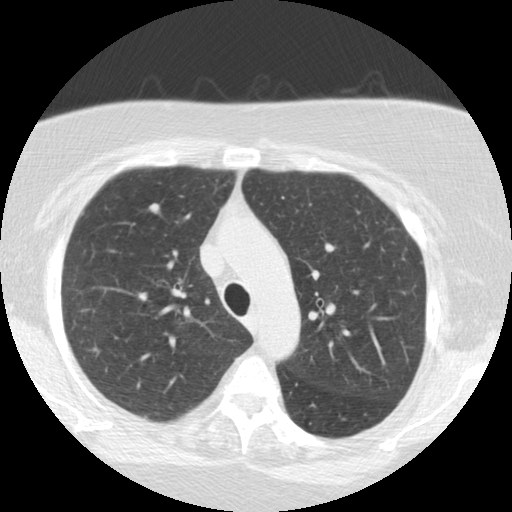
Chest CT (low-dose screening protocol), one axial image. Second annual screen. Lung window (W 1500 / L -600 HU). Slice 171 of 225 in the series. 512 × 512 image matrix. Female participant, aged 64 years at enrolment.
Lesion marked by an expert reader, box from (x=128, y=193) to (x=170, y=230) px. The exam's reader record, not a measurement of the box and not confirmed to be the same lesion: non-calcified nodule or mass ≥4 mm, right upper lobe, 8 × 7 mm, smooth margins, soft tissue attenuation, pre-existing on the prior screen: no. Participant outcome: lung cancer diagnosed 85 days after this screen — large cell neuroendocrine carcinoma, right upper lobe, stage IA (AJCC 6th edition), 12 mm at pathology.